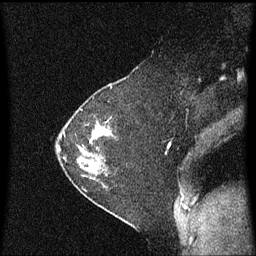
Breast MRI (dynamic contrast-enhanced), one sagittal slice. Position 40 of 60 along the scan axis. Dynamic contrast-enhanced series, image 2 of 3 at this slice position (ordered by acquisition). 1.5 T. TE 4.2 ms, TR 8.4 ms. 2 mm slice thickness. 256 × 256 image matrix, field of view 200 × 200 mm. Female patient, age 36 years. Case-level facts recorded for this patient, not image findings: setting: breast cancer imaged before/during neoadjuvant chemotherapy; receptor status: HR-positive, HER2-negative.
Structures marked on this image (semi-automatically segmented with operator editing):
- analysis volume of interest (the breast-tissue region the enhancement analysis was run in; not a lesion): bounding box [x1, y1, x2, y2] px = [66, 102, 113, 179]
- tumour enhancement mask (voxels above the 70 % enhancement threshold inside the analysis volume of interest): [86, 122, 110, 171]